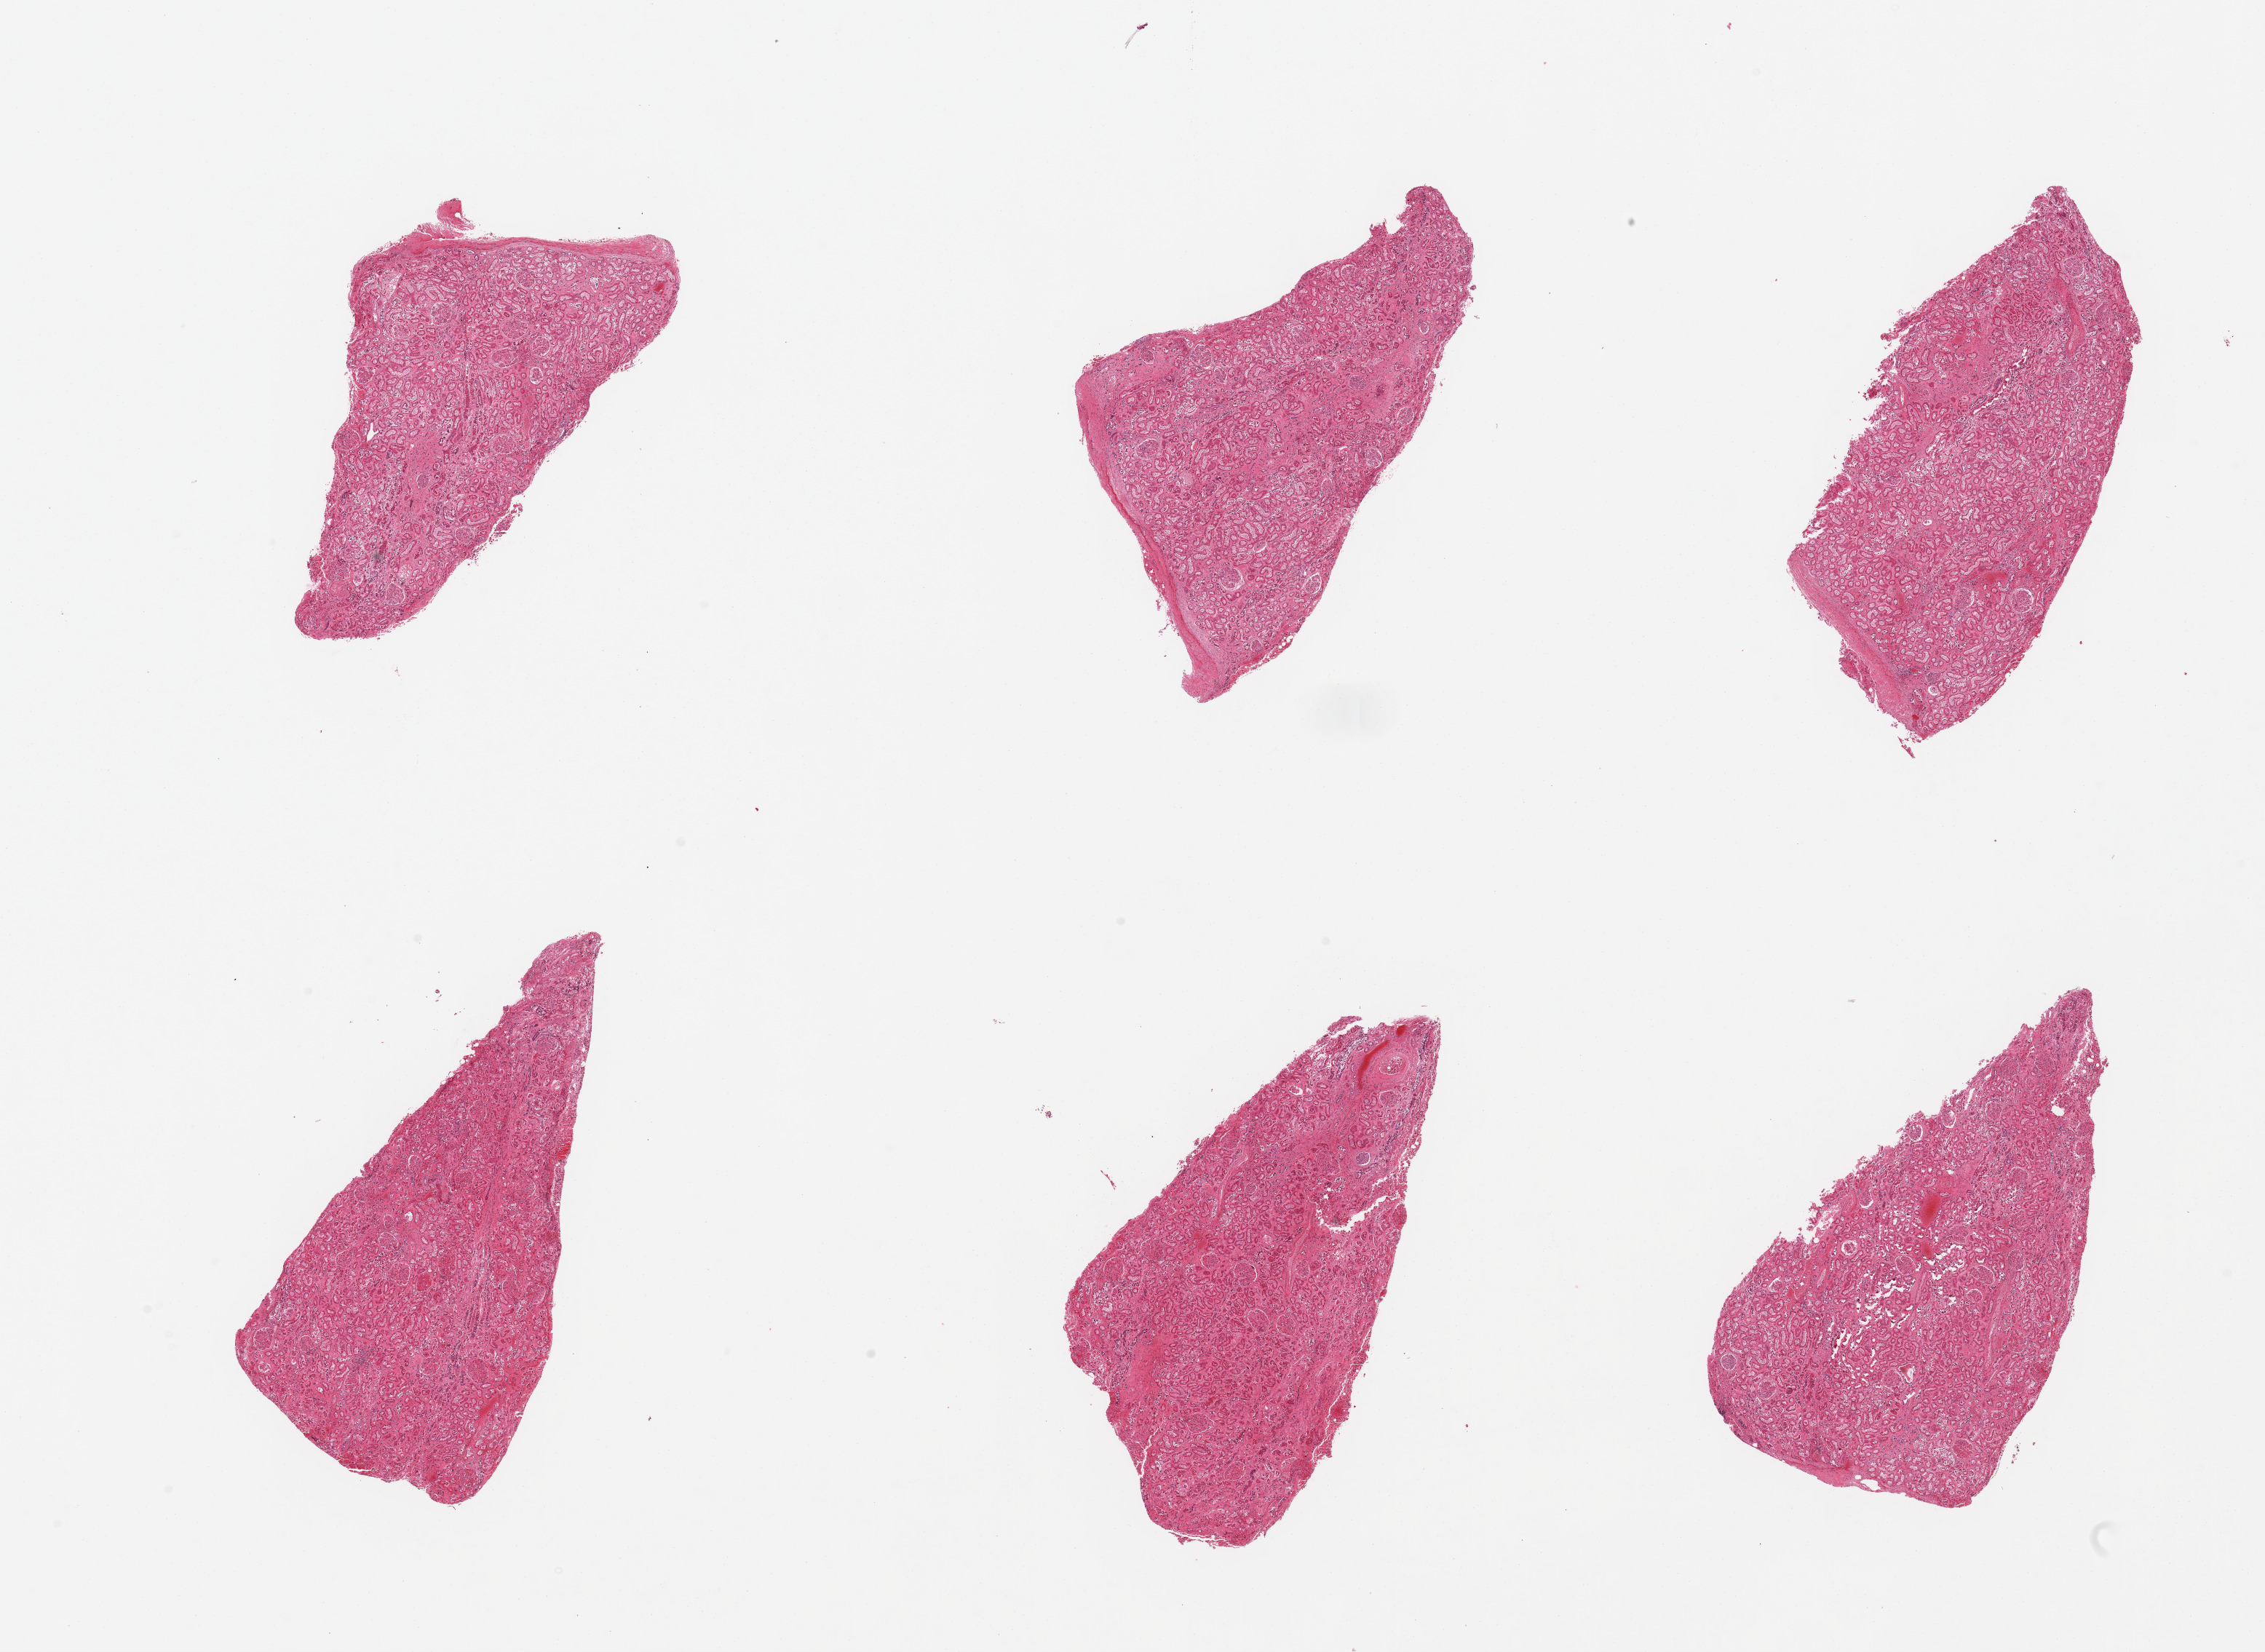
H&E whole-slide image — low-resolution overview of the scanned area, about 24.6 x 18.0 mm (acquisition: 20x scan), PAXgene-fixed paraffin-embedded (PFPE) section, section of renal cortex (target tissue), tissue donor sample. Male donor.
* pathologist's review note for this sample: 6 pieces, glomeruli present; tubules moderately autolyzed